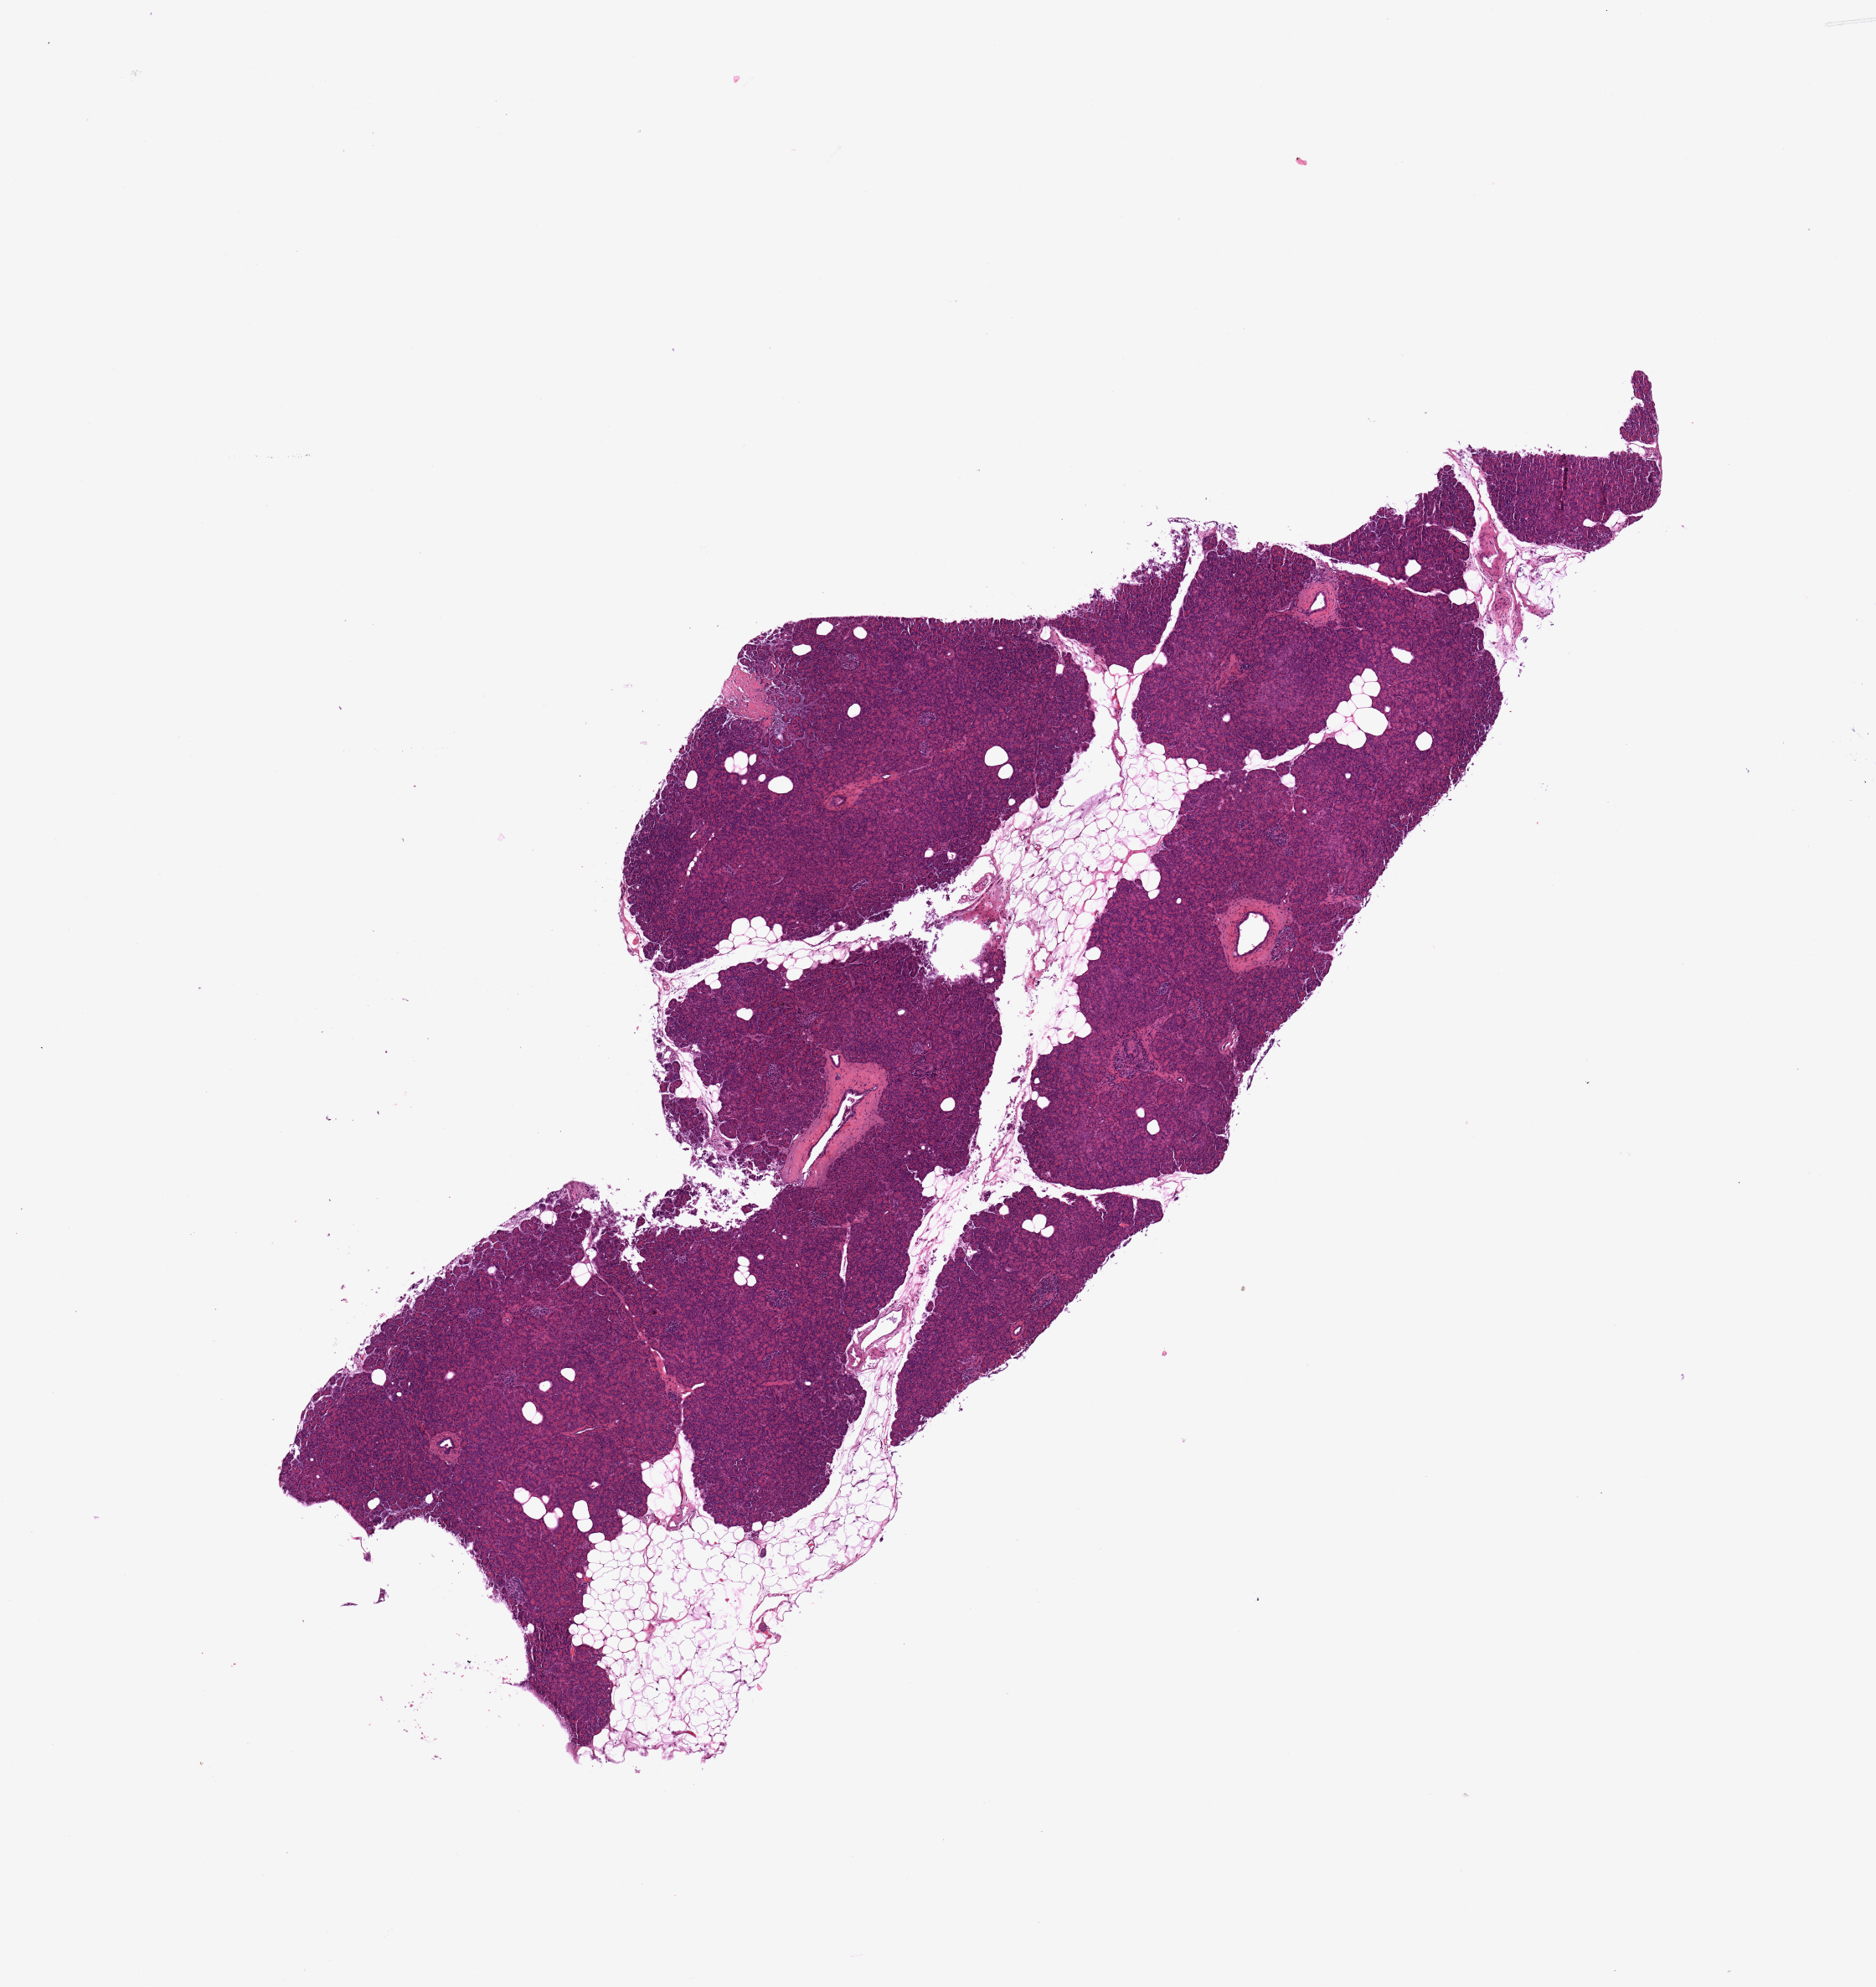
H&E-stained whole-slide image, a low-resolution overview of the entire scanned area, about 8.9 x 9.4 mm. Pancreas, normal (non-tumour) tissue. Patient: male, age 80 years.
• this section: normal (non-tumour) tissue from the same patient
• patient diagnosis: Infiltrating duct carcinoma, NOS